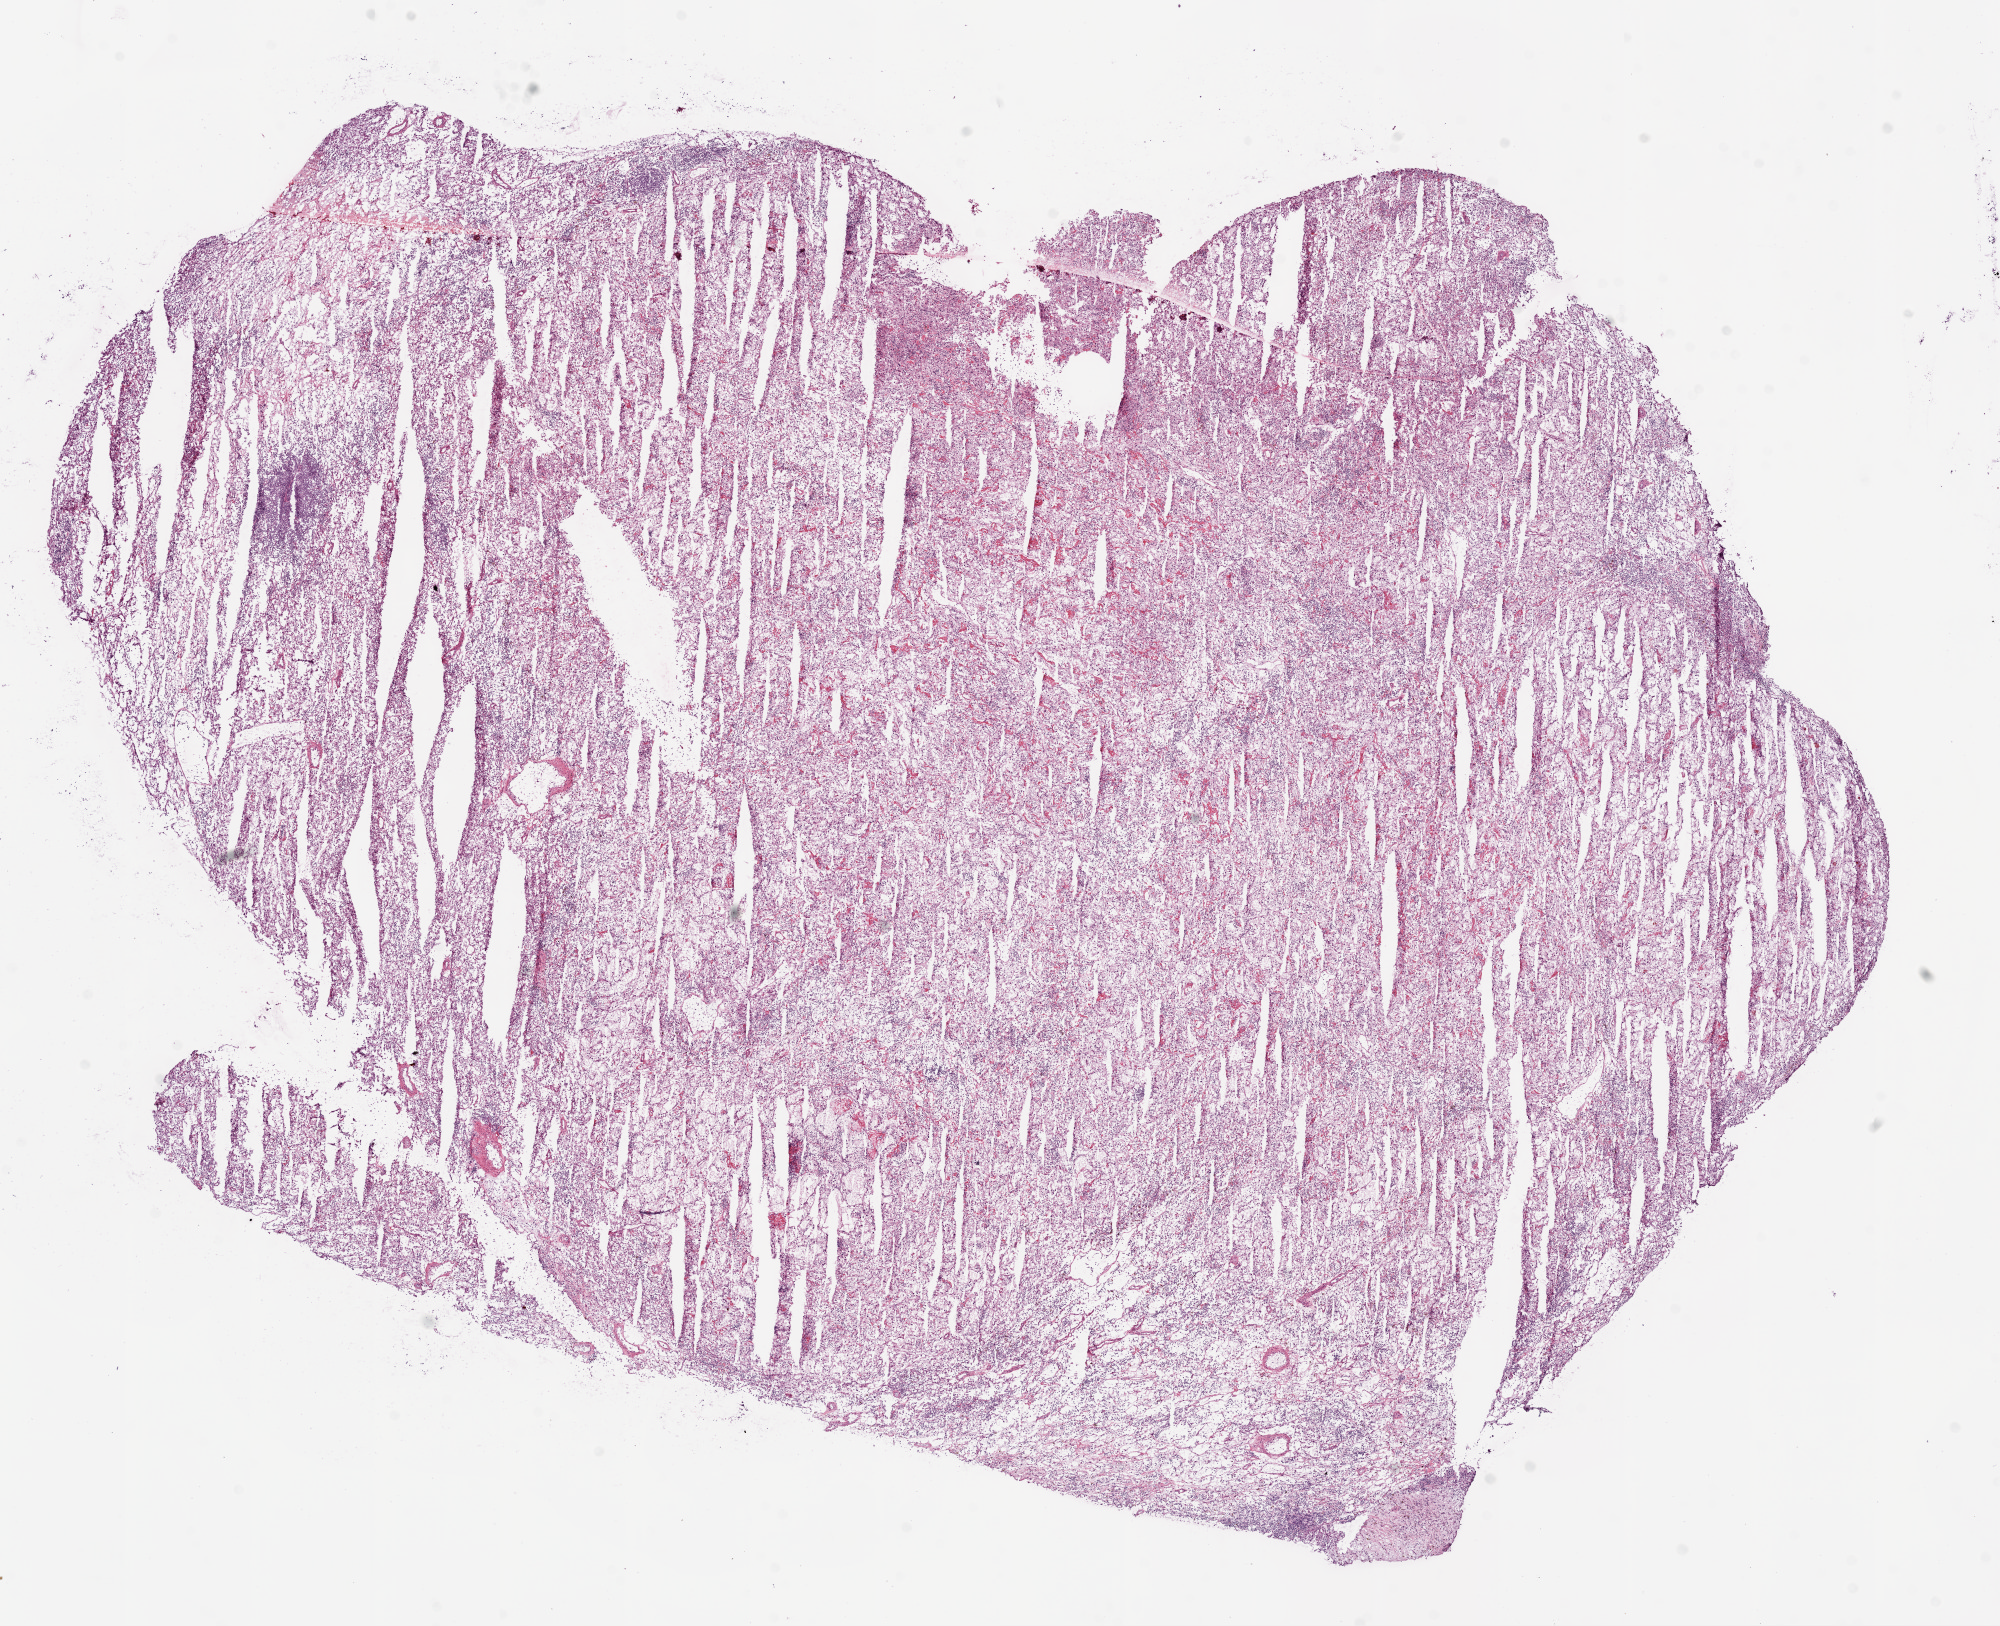
Whole-slide histology image, H&E — low-resolution overview of the scanned area, about 16.0 x 13.0 mm (from a 20x scan). Frozen section from the bottom of the tissue portion. Sample: primary tumour, kidney. Patient: male, age at initial diagnosis 72 years. Histologic grade: G2 (moderately differentiated). Composition of this section per pathologist review: tumour cells 95%, tumour nuclei 85%, normal cells 0%, stromal cells 5%, necrosis 0%.
- AJCC pathologic stage: I
- laterality: right
- diagnosis: Clear cell adenocarcinoma, NOS